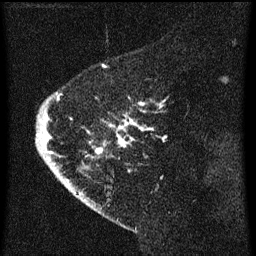
Breast MRI (dynamic contrast-enhanced), one sagittal slice. Position 15 of 60 along the scan axis. Dynamic contrast-enhanced series, image 2 of 3 at this slice position (ordered by acquisition). 1.5 T. TE 4.2 ms, TR 8 ms. 256 × 256 image matrix, field of view 180 × 180 mm. Female patient, age 47 years.
Outlined on this slice (semi-automatically segmented with operator editing):
- analysis volume of interest (the breast-tissue region the enhancement analysis was run in; not a lesion): box from (x=38, y=76) to (x=165, y=193) px
- tumour enhancement mask (voxels above the 70 % enhancement threshold inside the analysis volume of interest): (x=44, y=92)–(x=165, y=185)